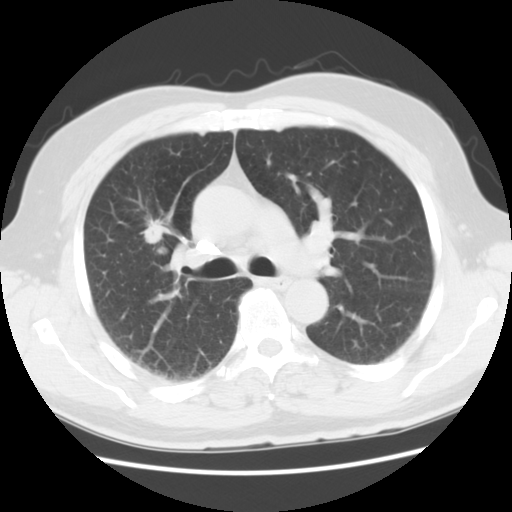
Chest CT (low-dose screening protocol), one axial image; second screening round (one year after baseline); lung window (W 1500 / L -600 HU); slice 27 of 70 in the series. Male participant, aged 59 years at enrolment. Current smoker at enrolment.
Expert reader's lesion annotation, box from (x=134, y=210) to (x=173, y=255) px. Screening reader's record for this exam (one nodule recorded; not confirmed to be the boxed lesion): non-calcified nodule or mass ≥4 mm, right upper lobe, 20 × 13 mm, spiculated (stellate) margins, soft tissue attenuation, pre-existing on the prior screen: yes; interval growth: yes. Lung cancer was diagnosed 267 days after this screen: large cell carcinoma, NOS, right upper lobe, poorly differentiated (G3), stage IIIA (AJCC 6th edition), 34 mm at pathology.